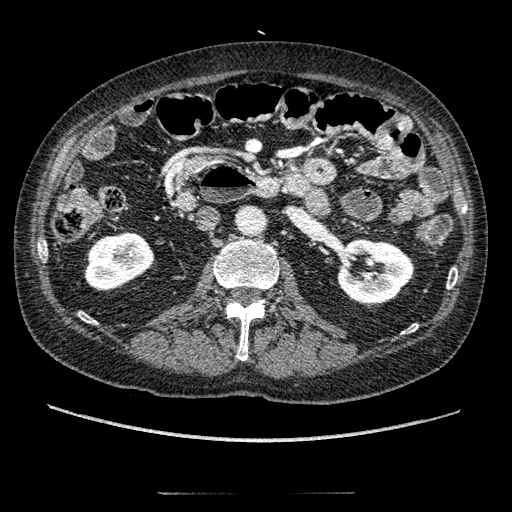
Contrast-enhanced abdominal CT, one axial slice; position 79 of 274 along the scan axis; 120 kVp; intravenous contrast given; soft-tissue window (W 400 / L 40 HU); 1.25 mm slice thickness; 512 × 512 image matrix, field of view 381 × 381 mm. Patient: male, 69 years. Case-level facts recorded for this patient, not image findings: diagnosis: adrenocortical carcinoma; tumour side: left adrenal; tumour size at pathology: 6.1 cm; Ki-67 index: 10 %; stage (as recorded): 3.
Structures marked on this image (semi-automatically segmented with operator editing):
- mass: bounding box [x1, y1, x2, y2] px = [307, 190, 327, 214]